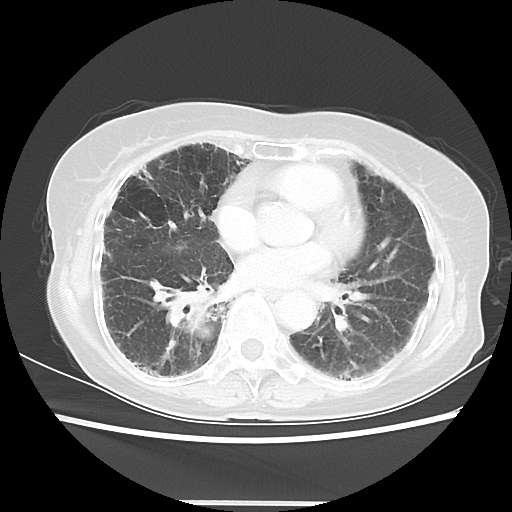
Chest CT, one axial slice. Slice 24 of 52 in the series (ordered by position). 120 kVp. Lung window (W 1500 / L -600 HU). 5 mm slice thickness. 512 × 512 image matrix, field of view 325 × 325 mm. Patient: female, 71 years. From the clinical record (not read from this slice): clinical TNM (as recorded): T3 N0 M0.
Outlined on this slice (bounding box drawn by a radiologist):
- lung tumour (recorded histology: squamous cell carcinoma): box from (x=160, y=287) to (x=222, y=353) px